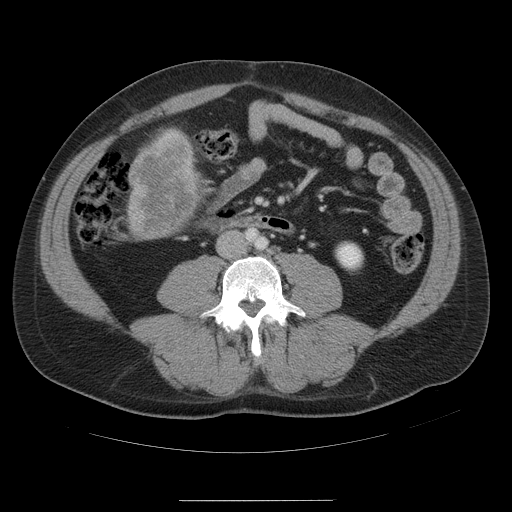
Contrast-enhanced abdominal CT, one axial slice. Position 7 of 54 along the scan axis. 120 kVp. Soft-tissue window (W 400 / L 40 HU). 512 × 512 image matrix, field of view 436 × 436 mm. Male patient, age 40 years. Case-level facts recorded for this patient, not image findings: diagnosis: colorectal cancer liver metastases, imaged before liver resection.
Annotated regions visible in this slice (manually delineated by an expert):
- liver: box from (x=127, y=131) to (x=203, y=240) px
- liver metastasis: (x=128, y=141)–(x=194, y=237)